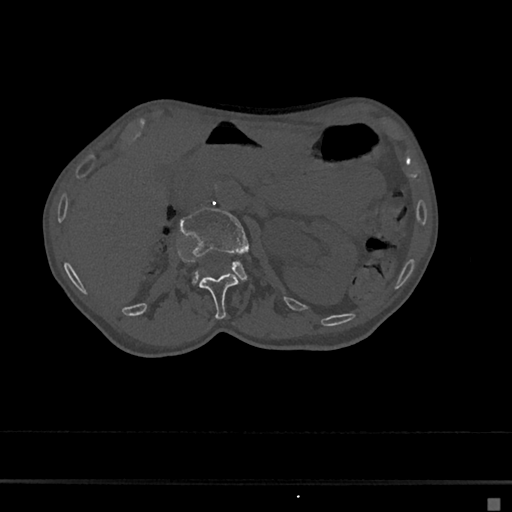
CT including the spine, one axial slice; slice 49 of 797 in the series (ordered by position); bone window (W 1800 / L 400 HU); 512 × 512 image matrix. Female patient, age 68 years. From the clinical record (not read from this slice): primary cancer: renal.
Annotated regions visible in this slice (semi-automatic segmentation, software-assisted and operator-edited):
- L1 vertebra: bounding box <199,273,237,320> (left, top, right, bottom; pixels)
- L2 vertebra: <180,208,250,281>